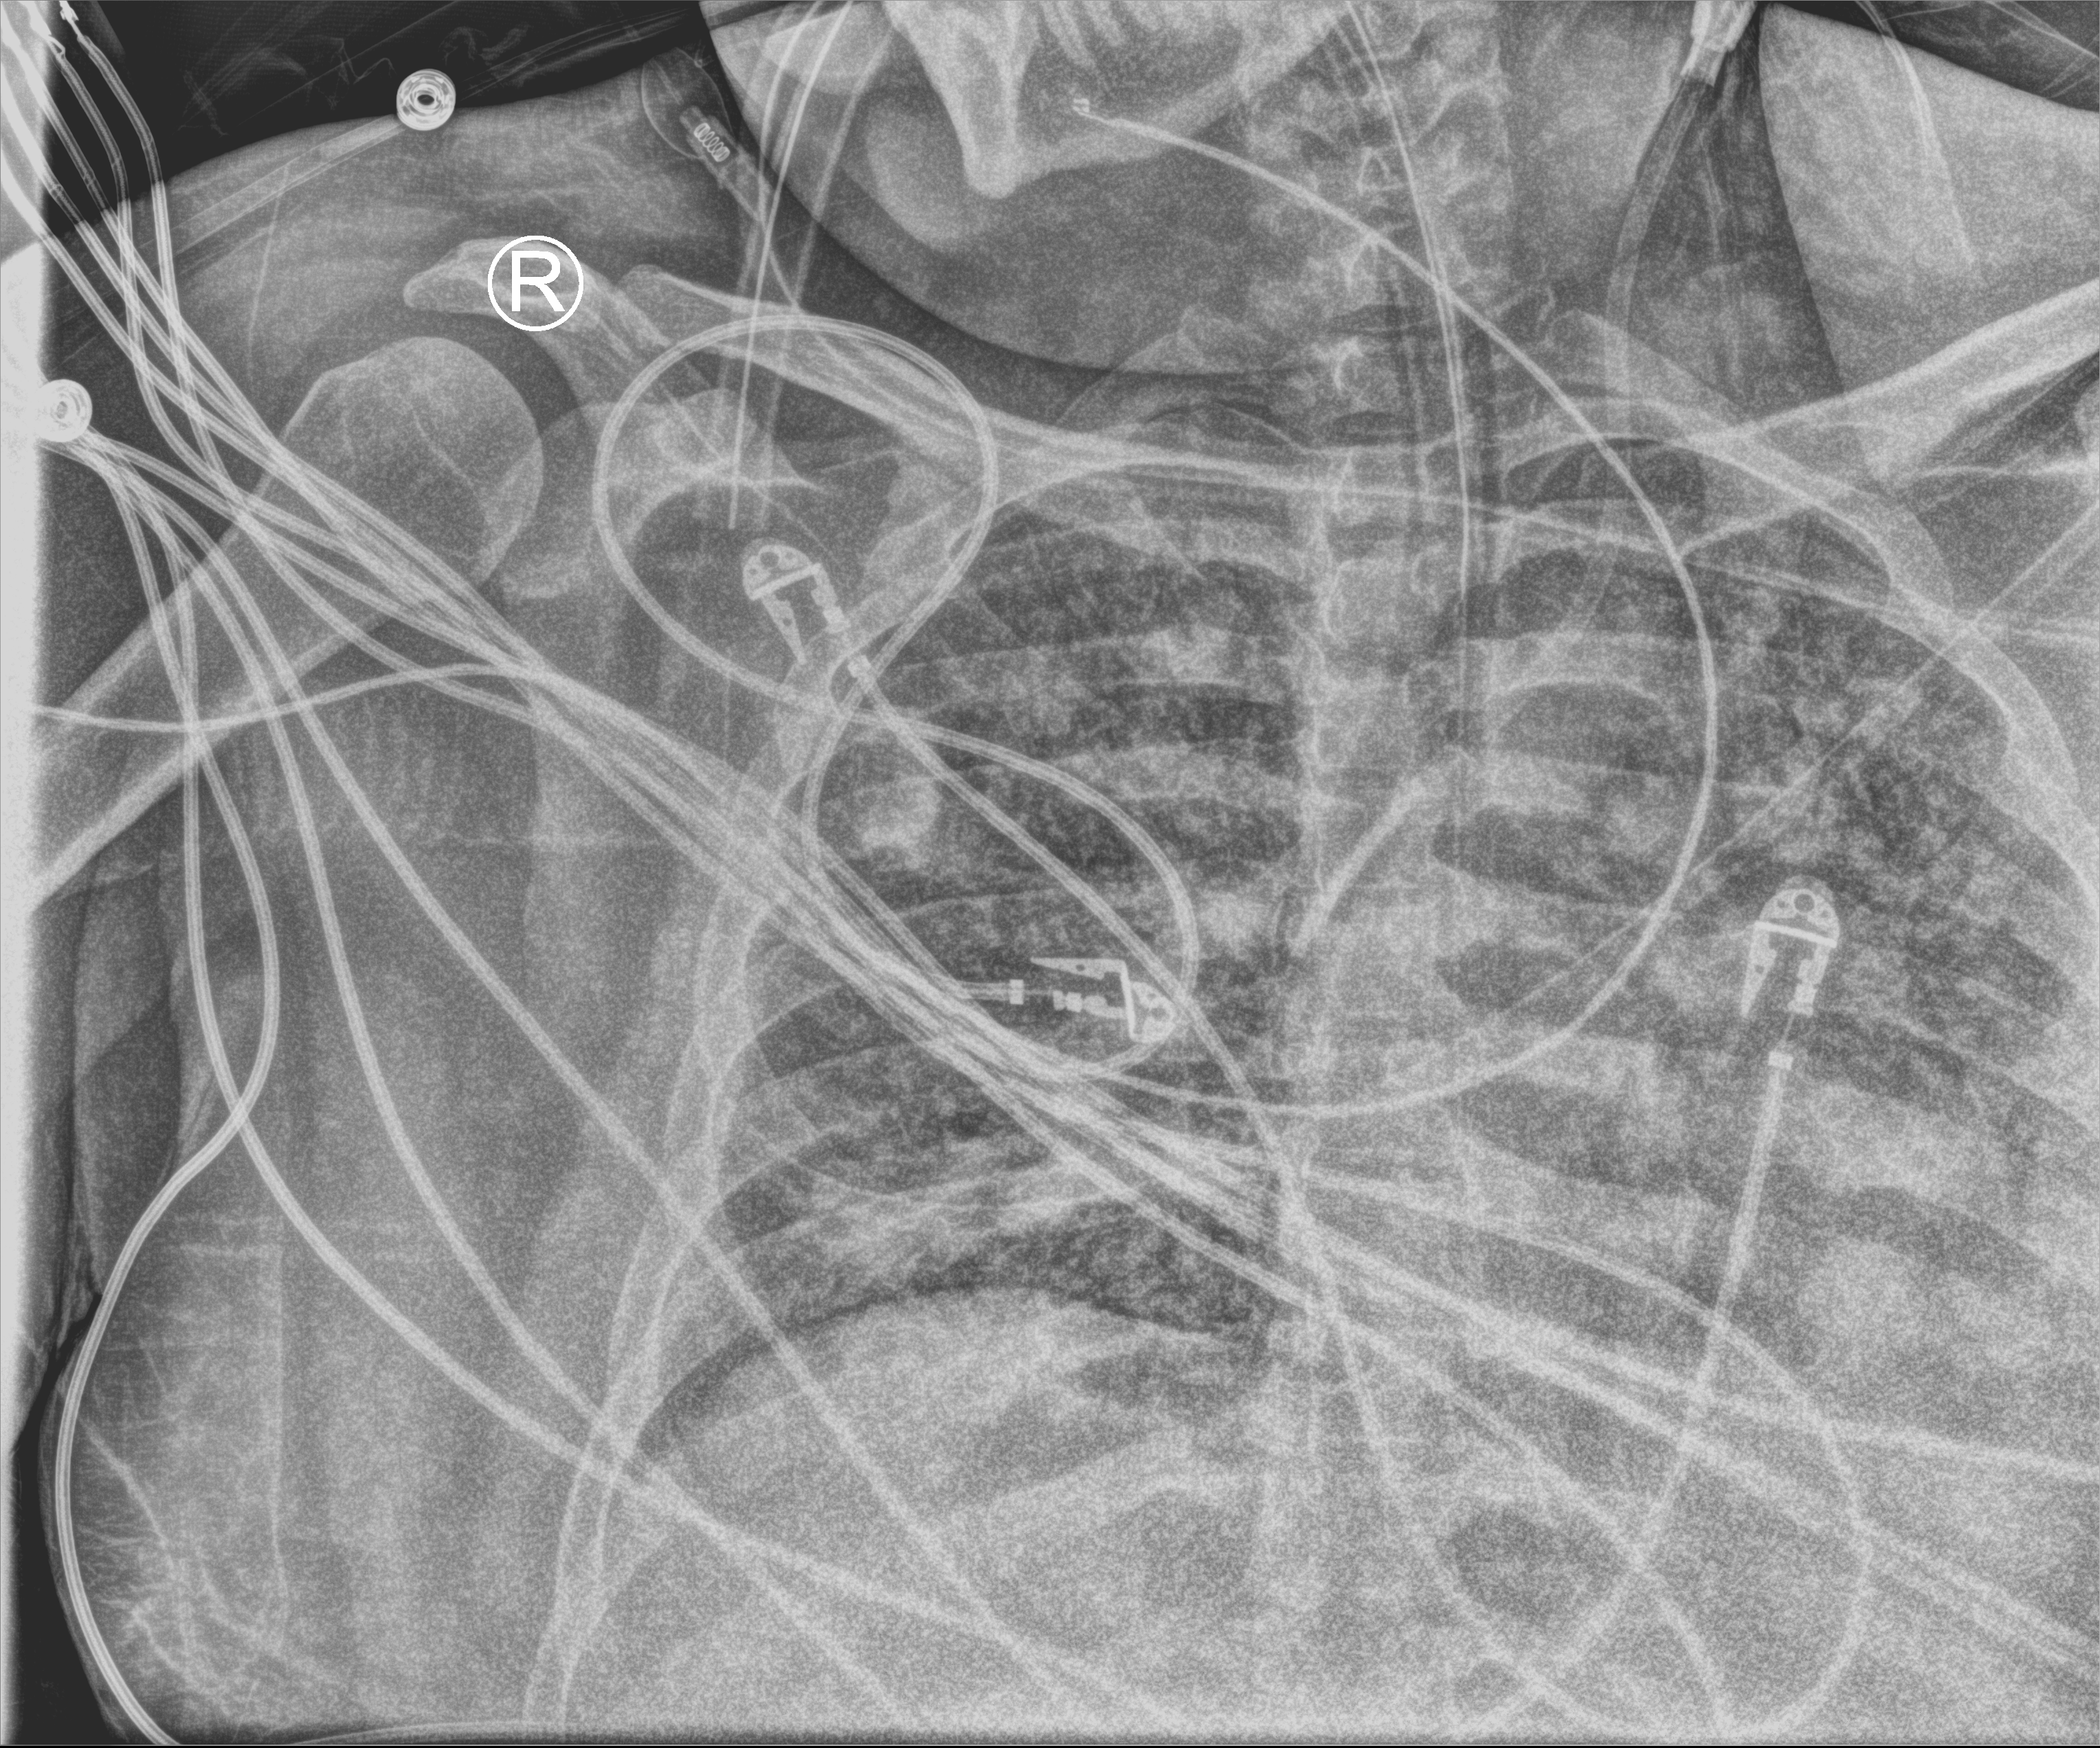
Chest X-ray (portable); anteroposterior (AP) projection. Adult patient hospitalised with COVID-19, age 18–59 years.
Admission-level facts for this patient (not findings on this image; timing relative to this image not recorded): length of hospital stay: 22 days; admitted to intensive care during this hospital stay: yes; chronic kidney disease (admission record): no.